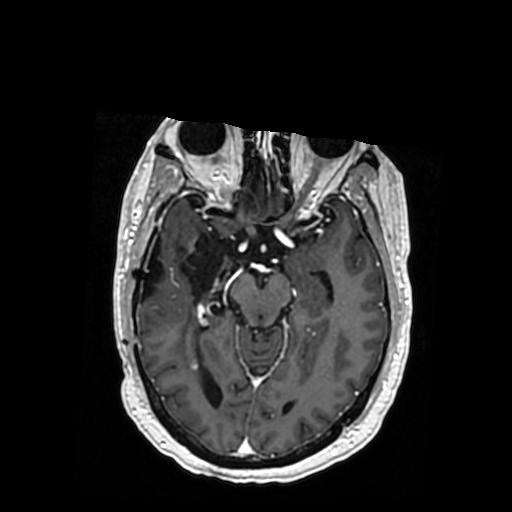
Brain MRI from a brain-tumour surgery series, one axial slice. Slice 212 of 364 in the series (ordered by position). T1-weighted post-contrast. 512 × 512 image matrix. From the clinical record (not read from this slice): histopathology: Oligodendroglioma; WHO grade: 3; IDH mutation: yes.
Structures marked on this image (manually delineated by an expert):
- previous resection cavity: bounding box [x1, y1, x2, y2] px = [141, 232, 239, 302]